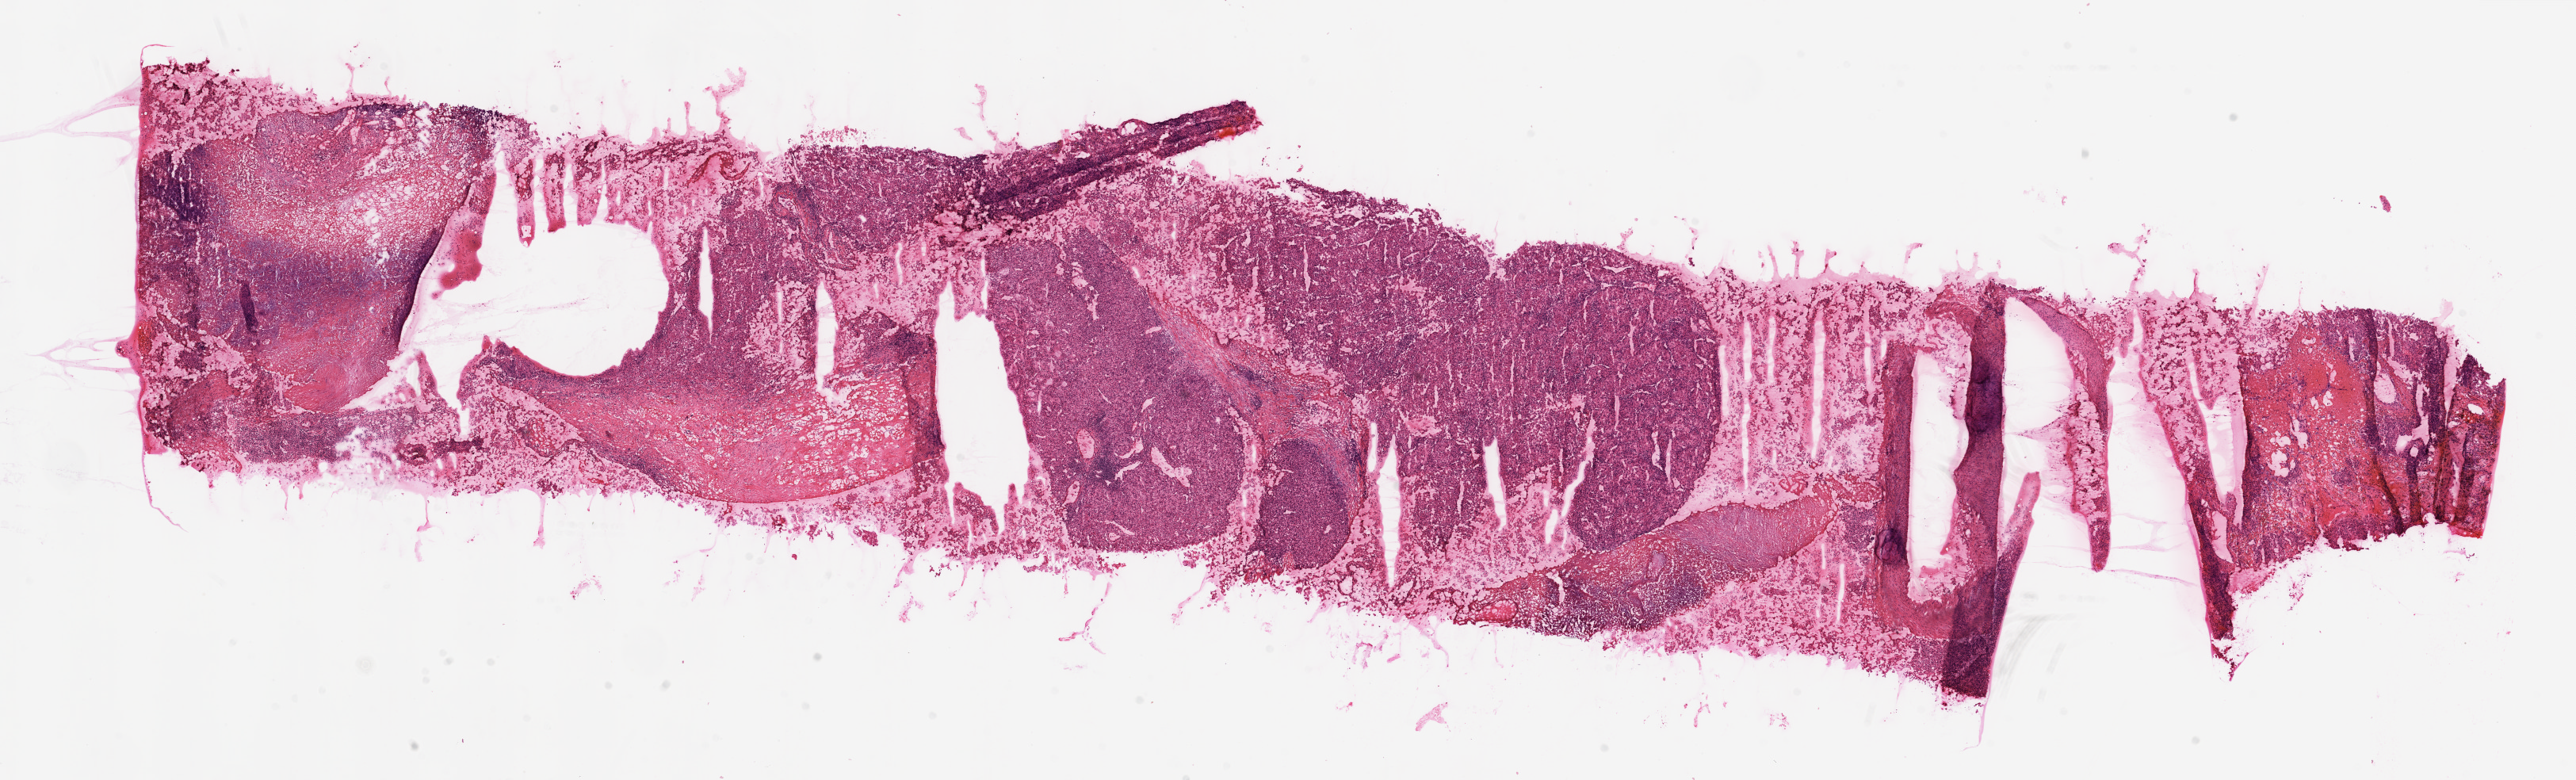
Whole-slide histology image, H&E, low-resolution overview of the scanned area, about 26.1 x 7.9 mm (from a 20x scan), frozen section, kidney, primary tumour sample. Male, age 59 years at initial diagnosis. Histologic grade: G4 (undifferentiated). Pathologist review of this section (percent, as recorded): tumour cells 90%, tumour nuclei 85%, normal cells 0%, stromal cells 10%, necrosis 0%.
AJCC pathologic stage: IV. Diagnosis: Clear cell adenocarcinoma, NOS.